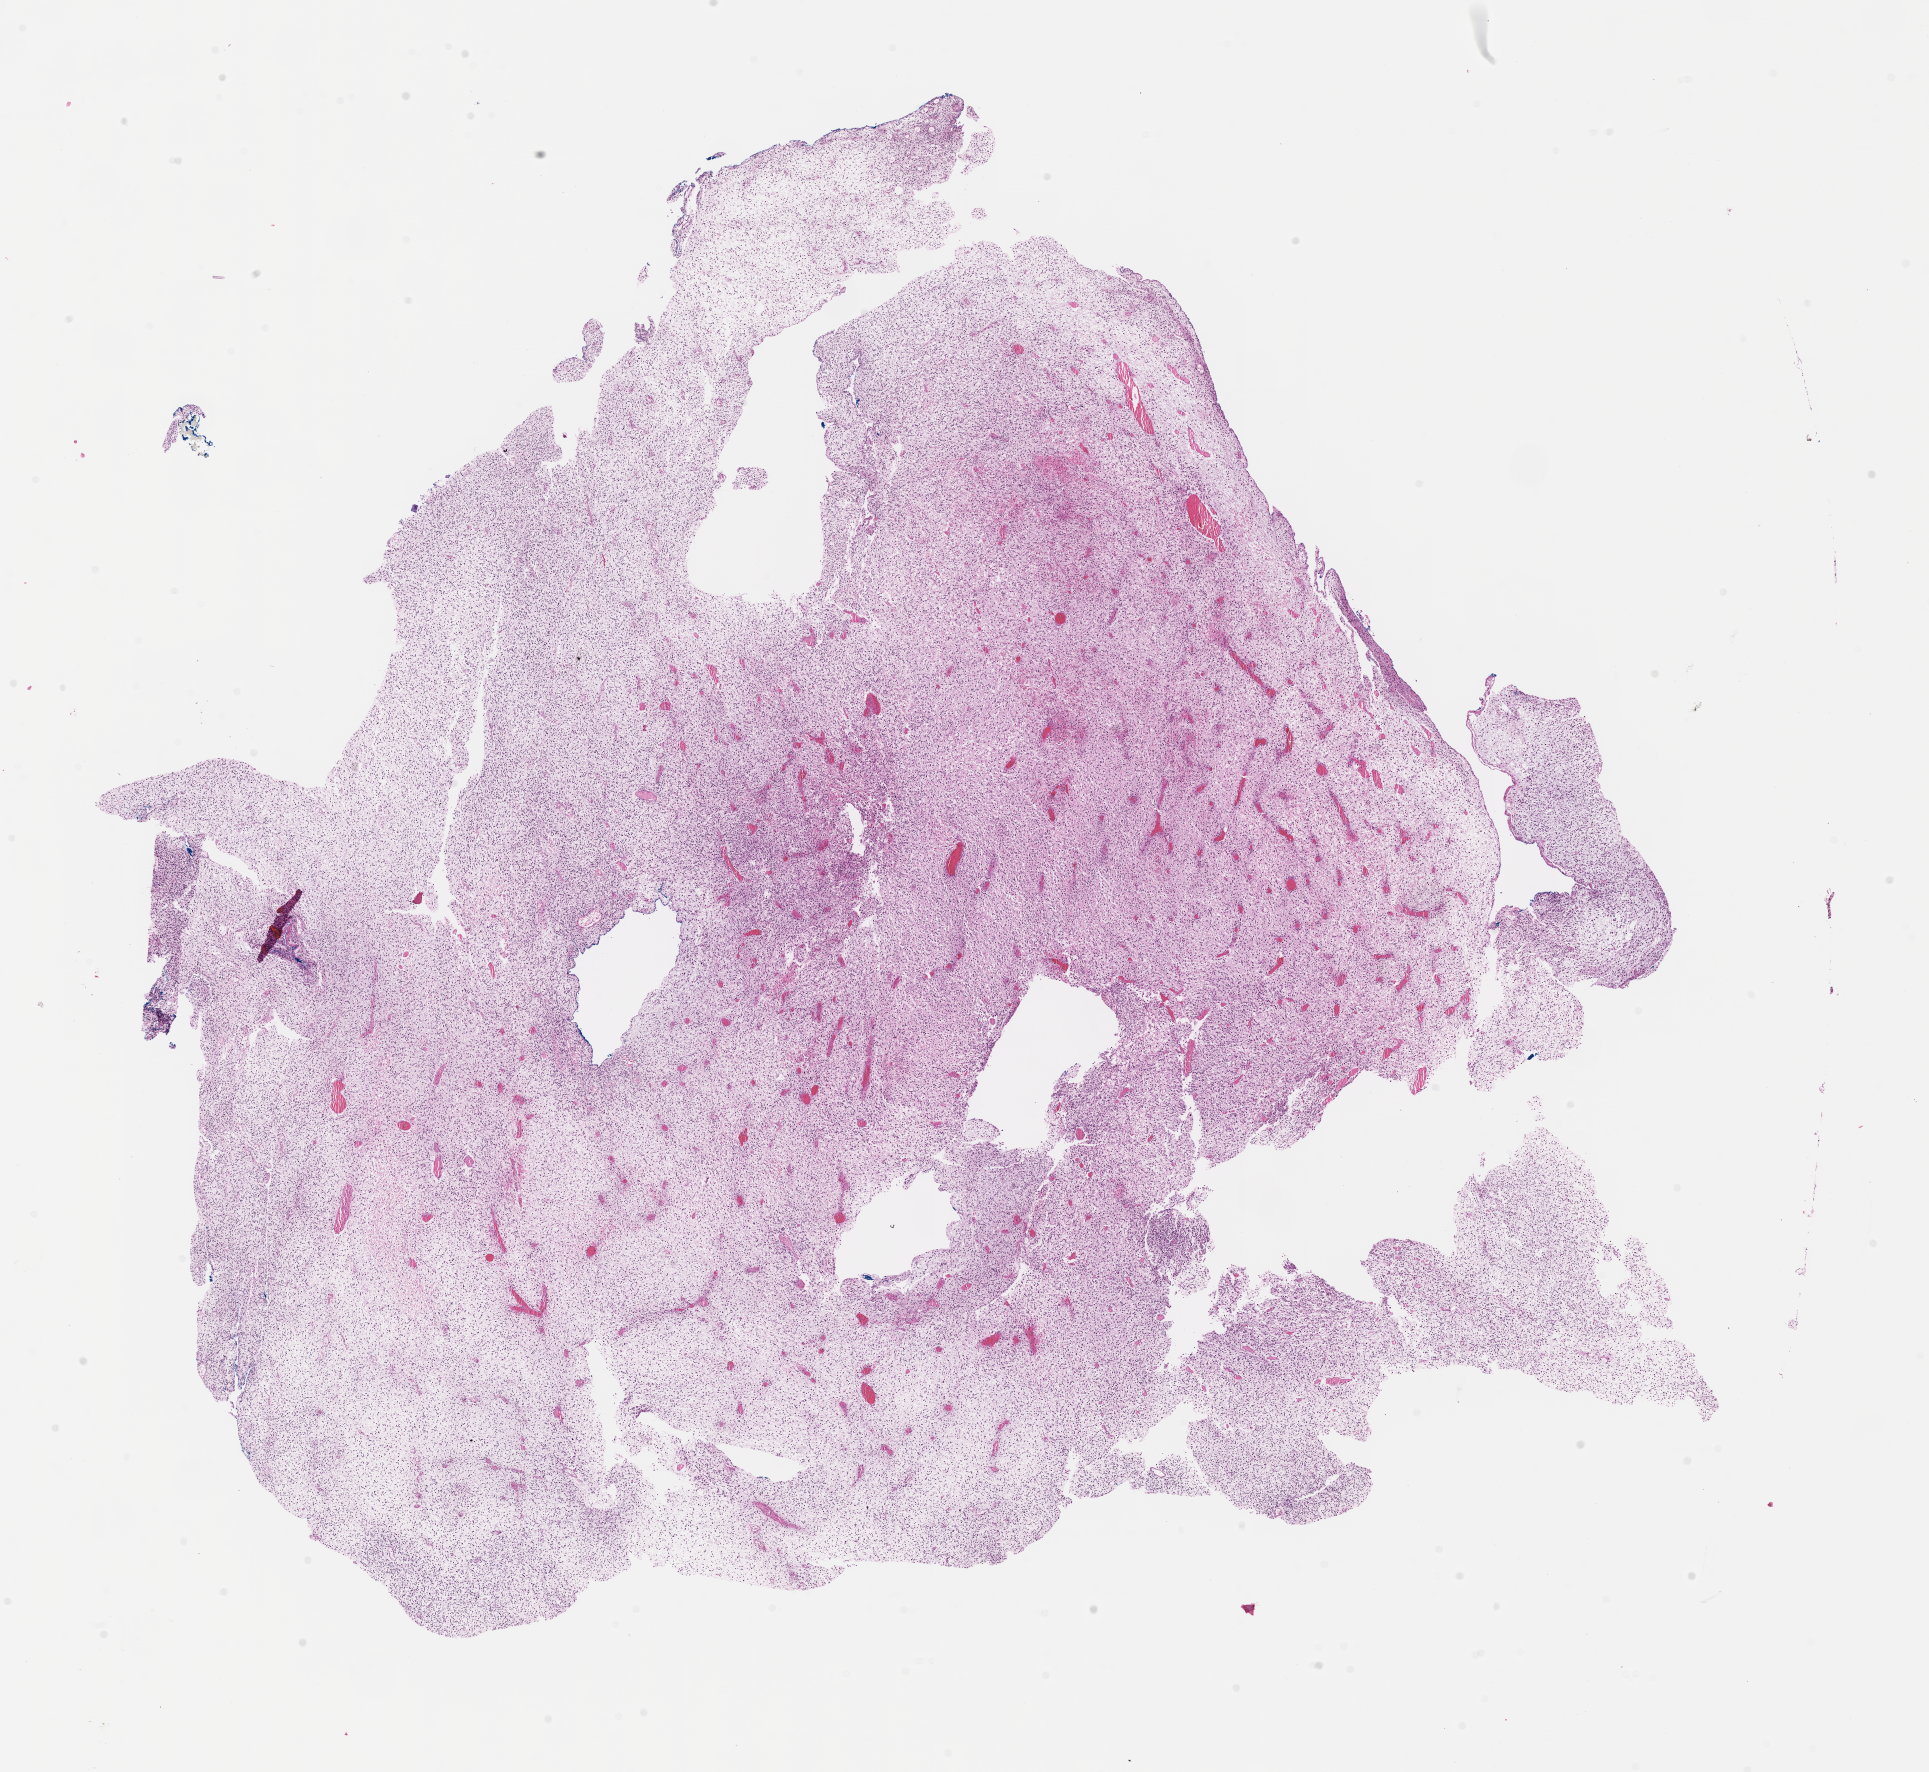
Whole-slide image, haematoxylin and eosin stain of tumor tissue — low-resolution overview of the scanned area, about 15.6 x 14.3 mm; FFPE section; sample anatomic site: abdomen. Patient: female, age 4.6 years at diagnosis.
* stage (as recorded): 4
* metastatic status at presentation (as recorded): metastatic (confirmed)
* diagnosis: rhabdomyosarcoma; histological classification: embryonal rhabdomyosarcoma